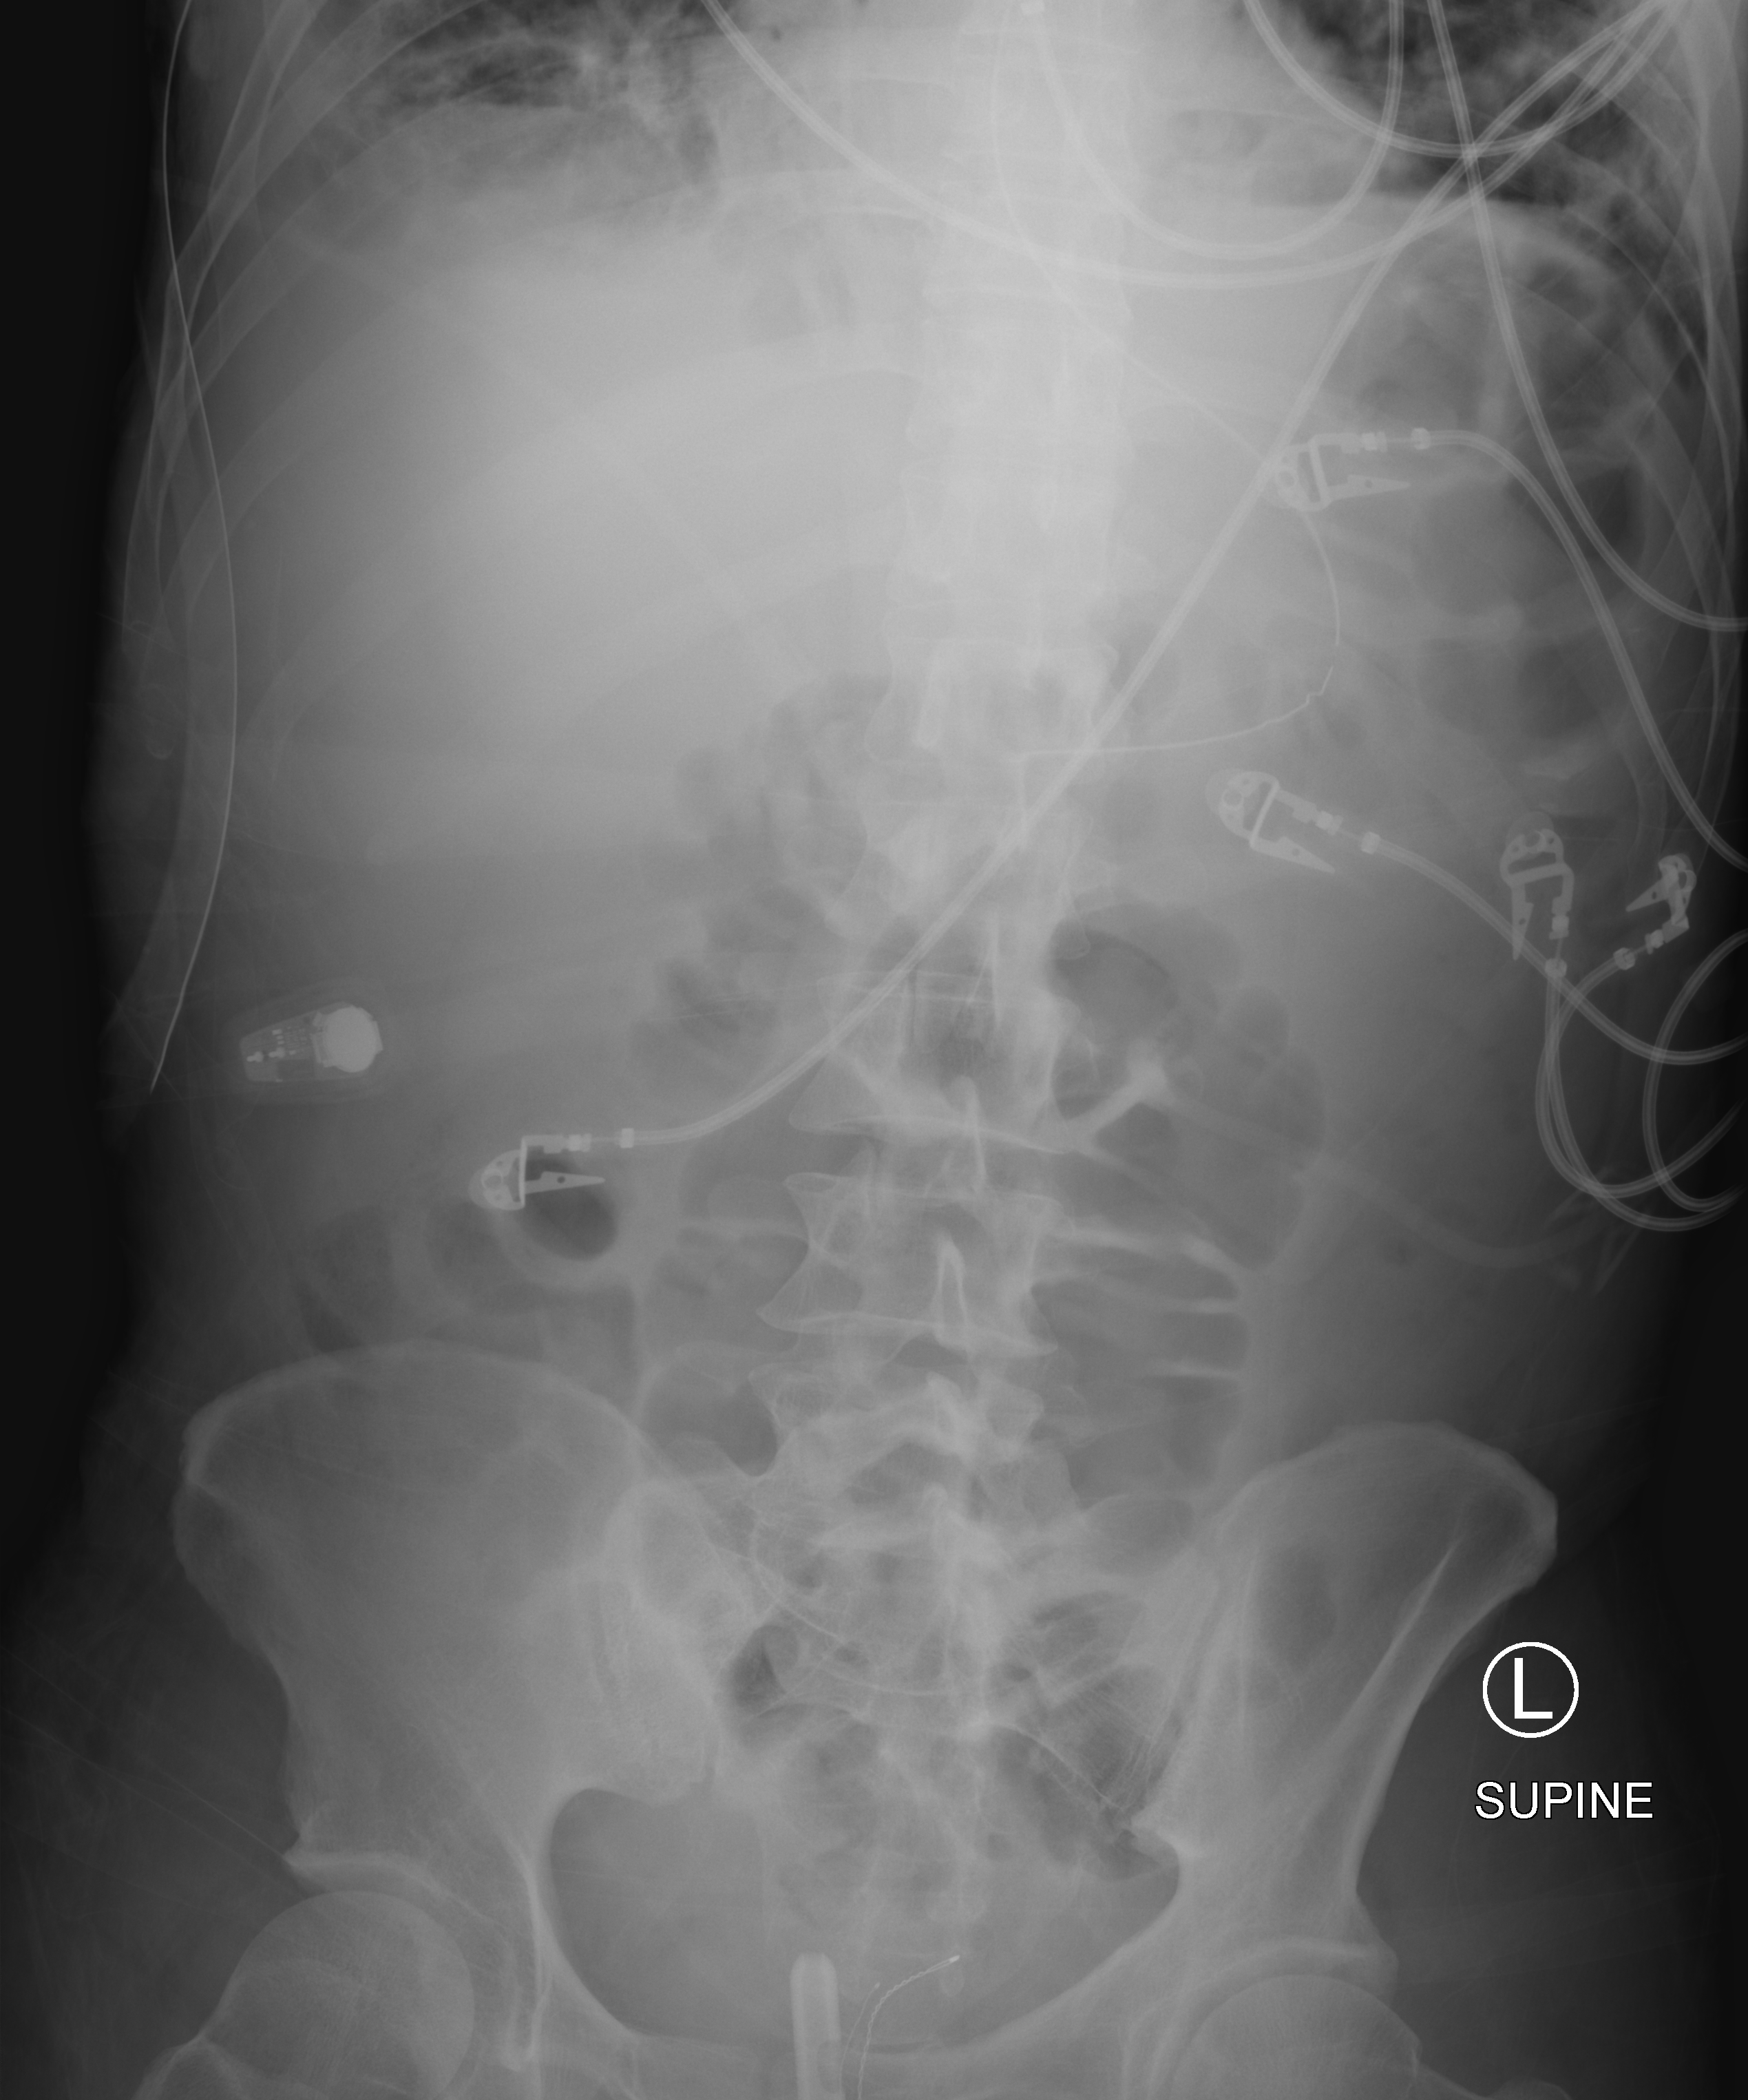
Portable abdomen radiograph; anteroposterior (AP) projection. Patient hospitalised with COVID-19; male, aged 18–59 years.
Admission-level facts for this patient (not findings on this image; timing relative to this image not recorded): chronic kidney disease (admission record): no; COPD (admission record): no; other chronic lung disease (admission record): no.